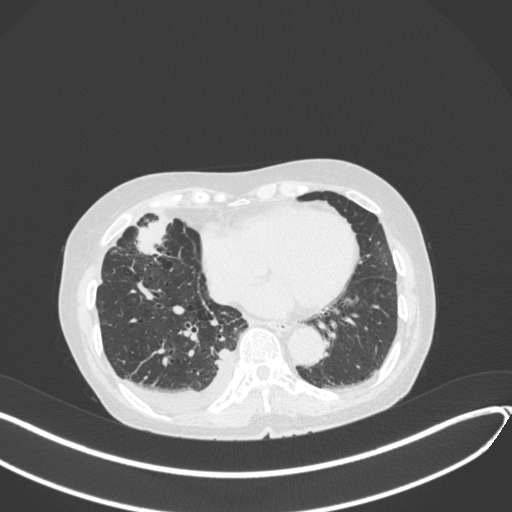
Chest CT, one axial slice; position 131 of 418 along the scan axis; reconstruction kernel B31f; 120 kVp; lung window (W 1500 / L -600 HU); 1 mm slice thickness; 512 × 512 image matrix, field of view 400 × 400 mm. Patient: female, 75 years. From the clinical record (not read from this slice): clinical TNM (as recorded): T2a N3 M0.
Annotated regions visible in this slice (rectangle marked by the reading radiologist):
- lung tumour (recorded histology: adenocarcinoma): bounding box (x1, y1, x2, y2) in pixels: (136, 207, 176, 257)